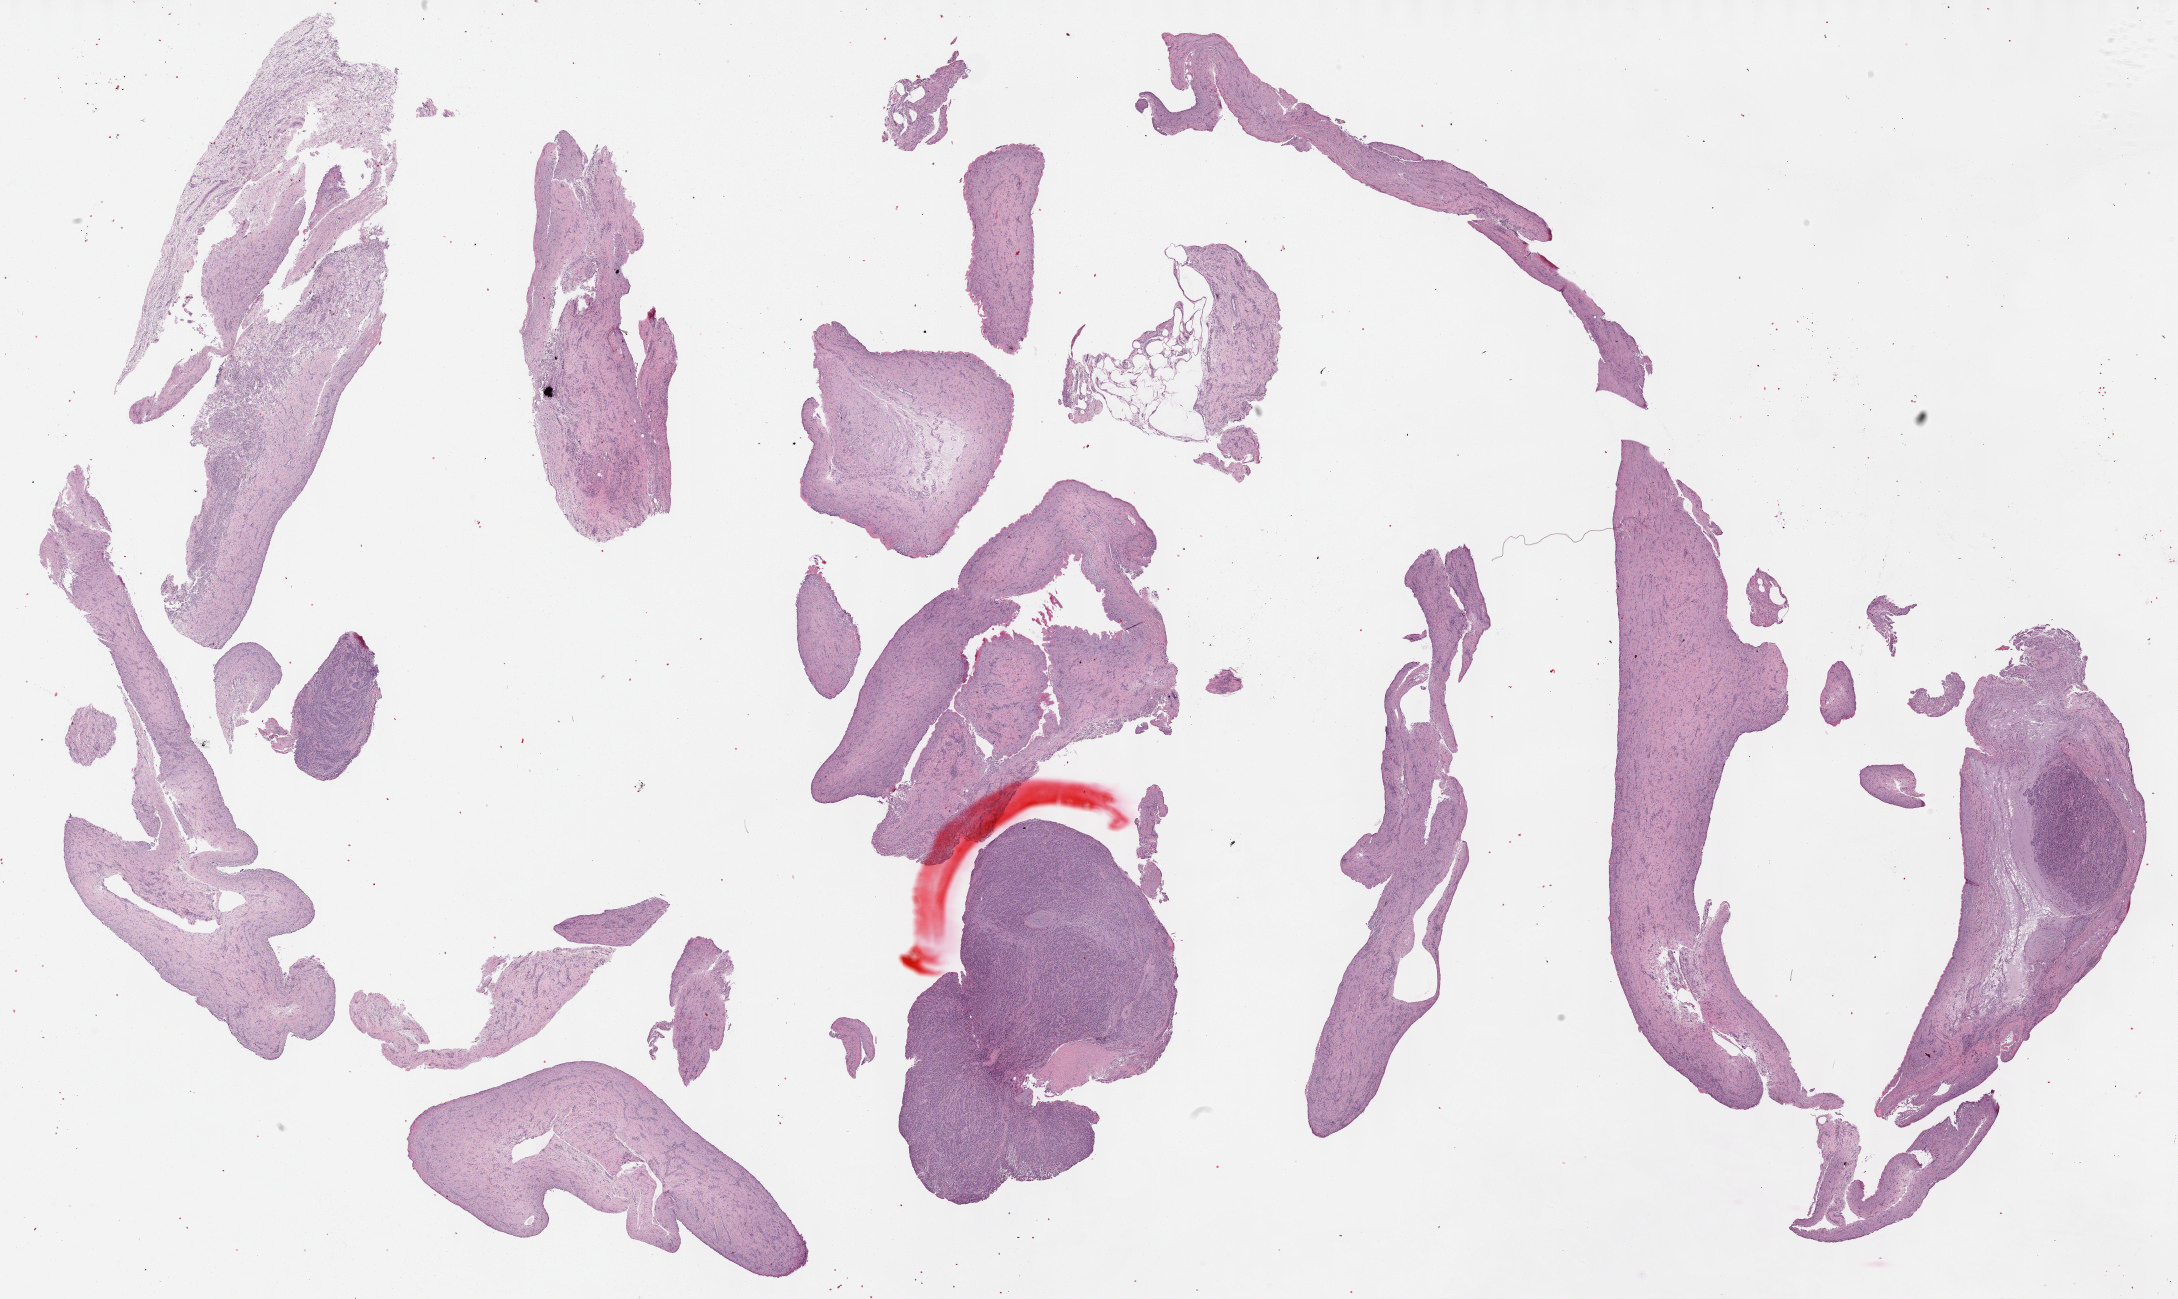
H&E whole-slide image — low-resolution overview of the scanned area, about 35.2 x 21.0 mm (acquisition: 40x scan); formalin-fixed paraffin-embedded (FFPE) diagnostic section; primary tumour sample from the mesothelium. Patient: male, age at initial diagnosis 54 years.
- histologic diagnosis: Epithelioid mesothelioma, malignant (pleura, NOS)
- AJCC pathologic stage: IV (7th edition)
- laterality: left